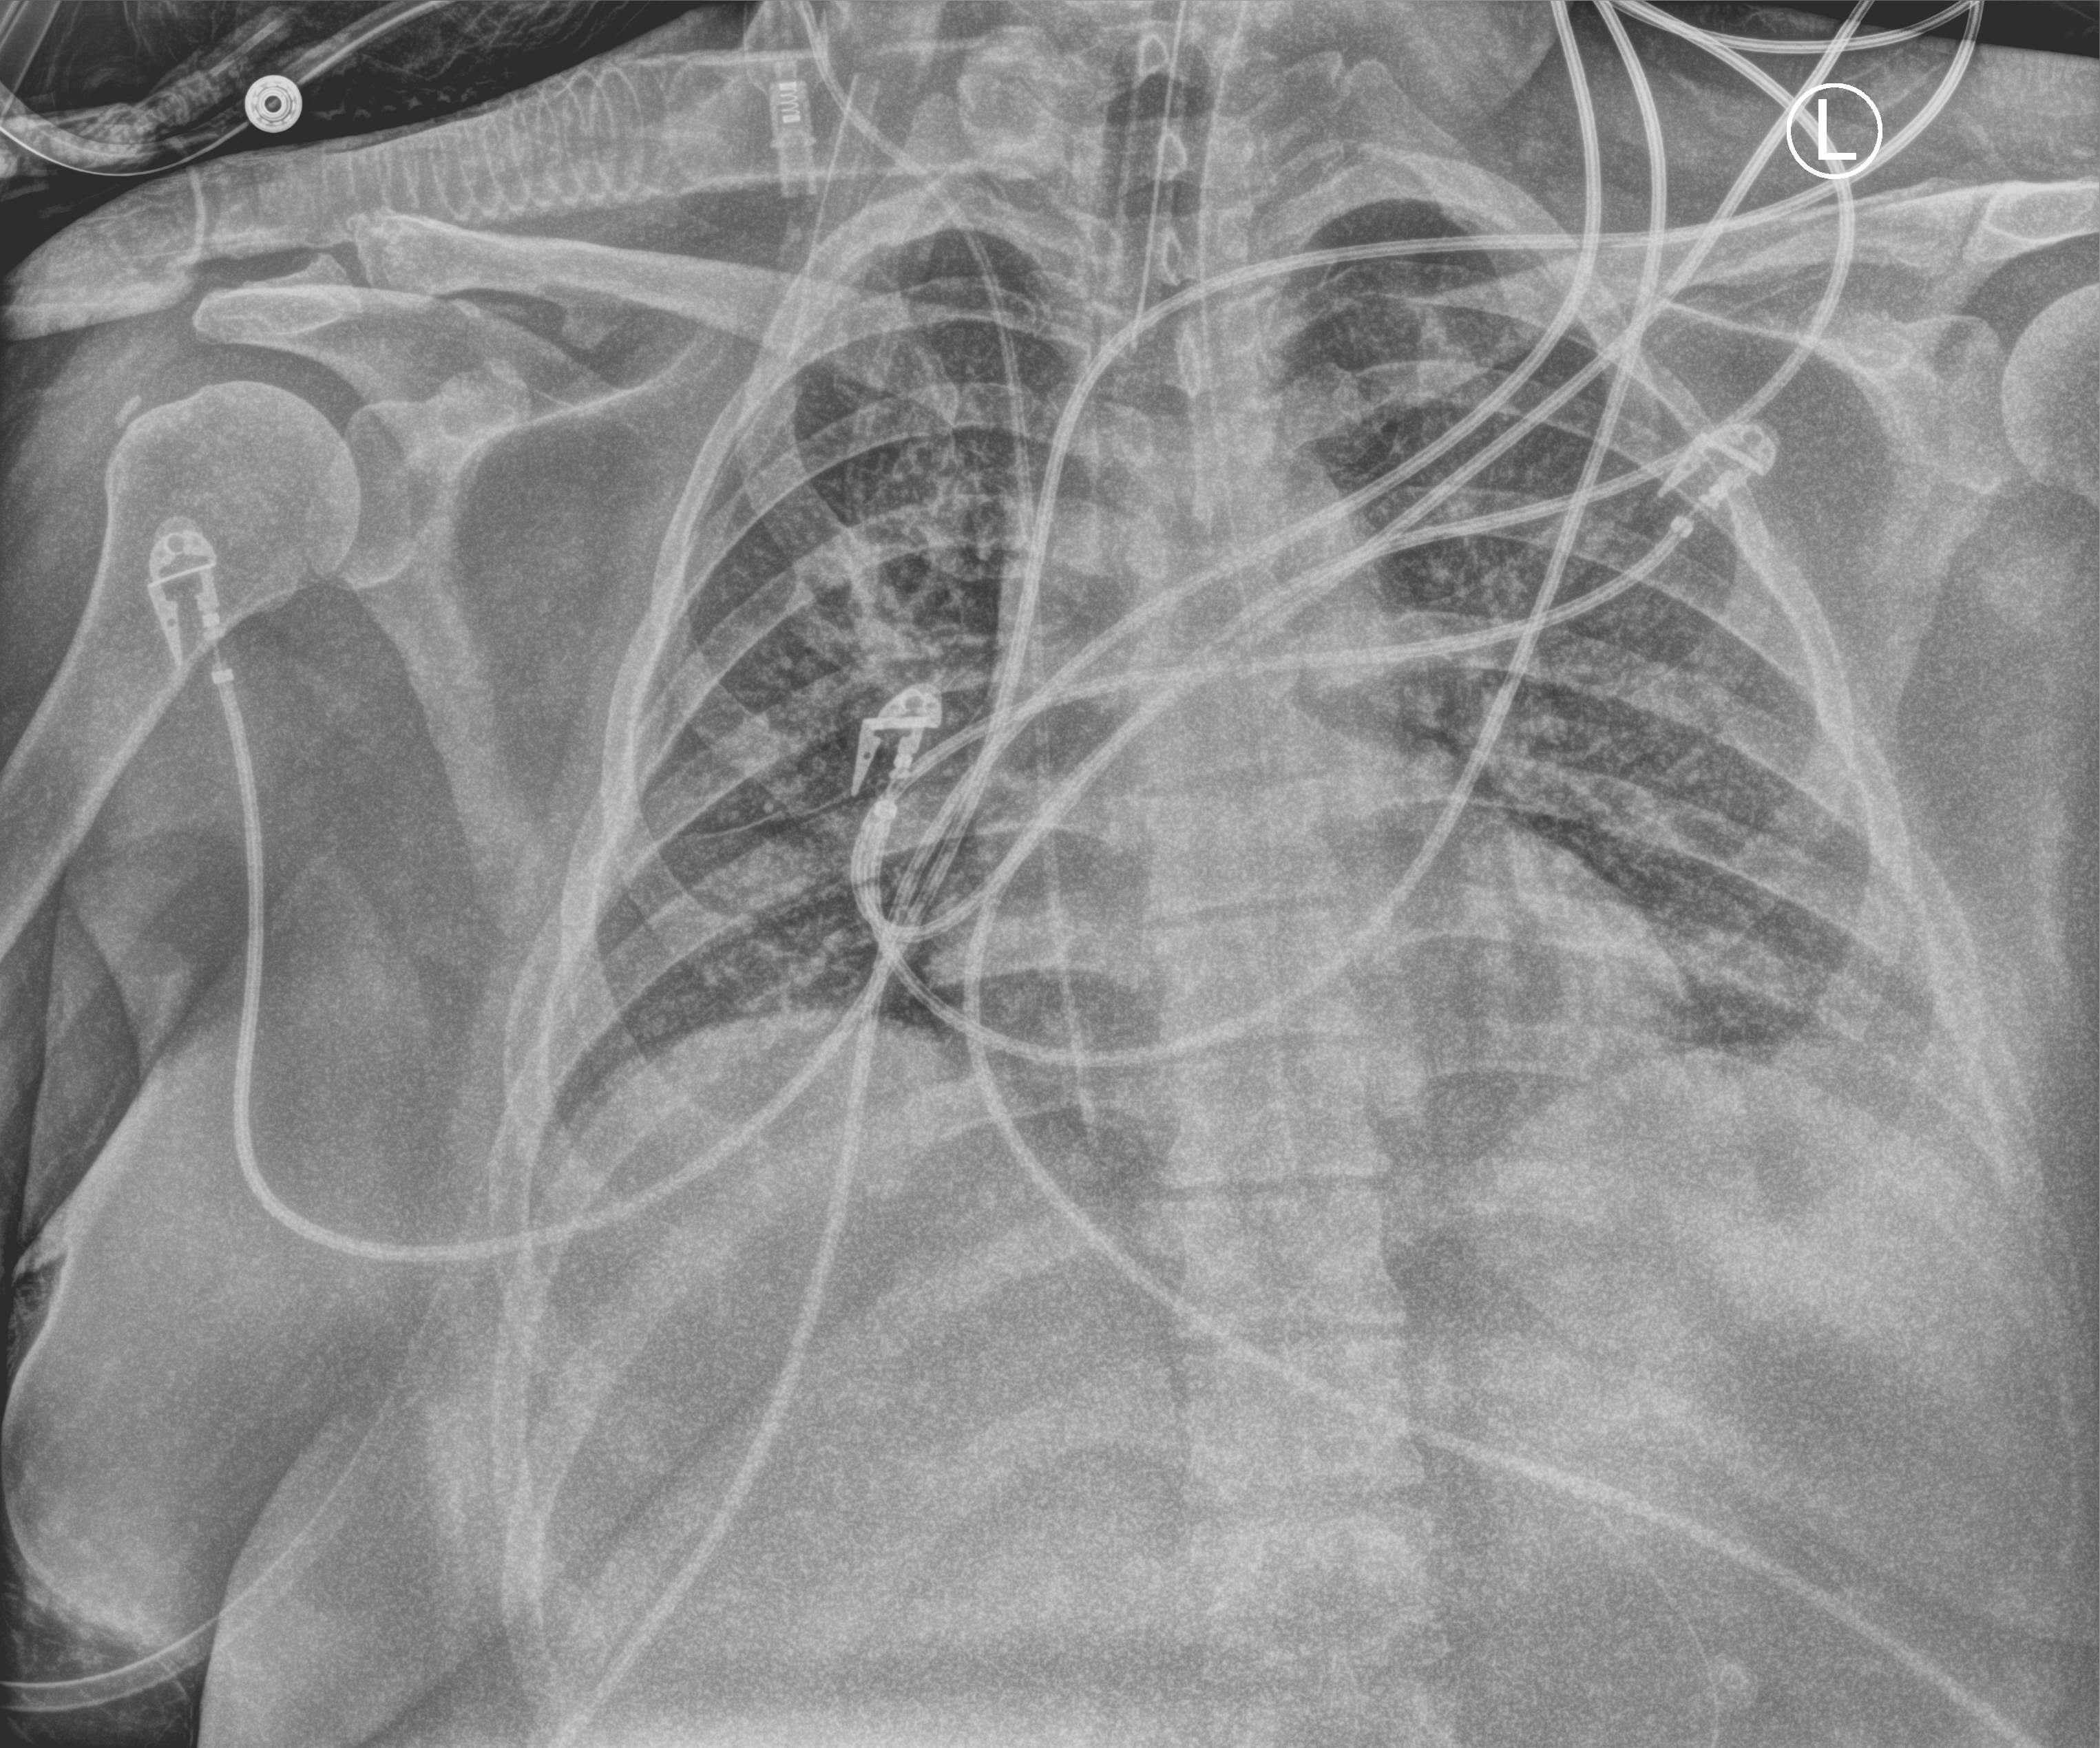
Chest X-ray (portable); anteroposterior (AP) projection. Female patient hospitalised with COVID-19, age 18–59 years.
From the hospital-stay record, not from the radiograph (when in the stay this image was taken is not recorded):
- mechanically ventilated during this hospital stay: yes
- length of hospital stay: 25 days
- admitted to intensive care during this hospital stay: yes